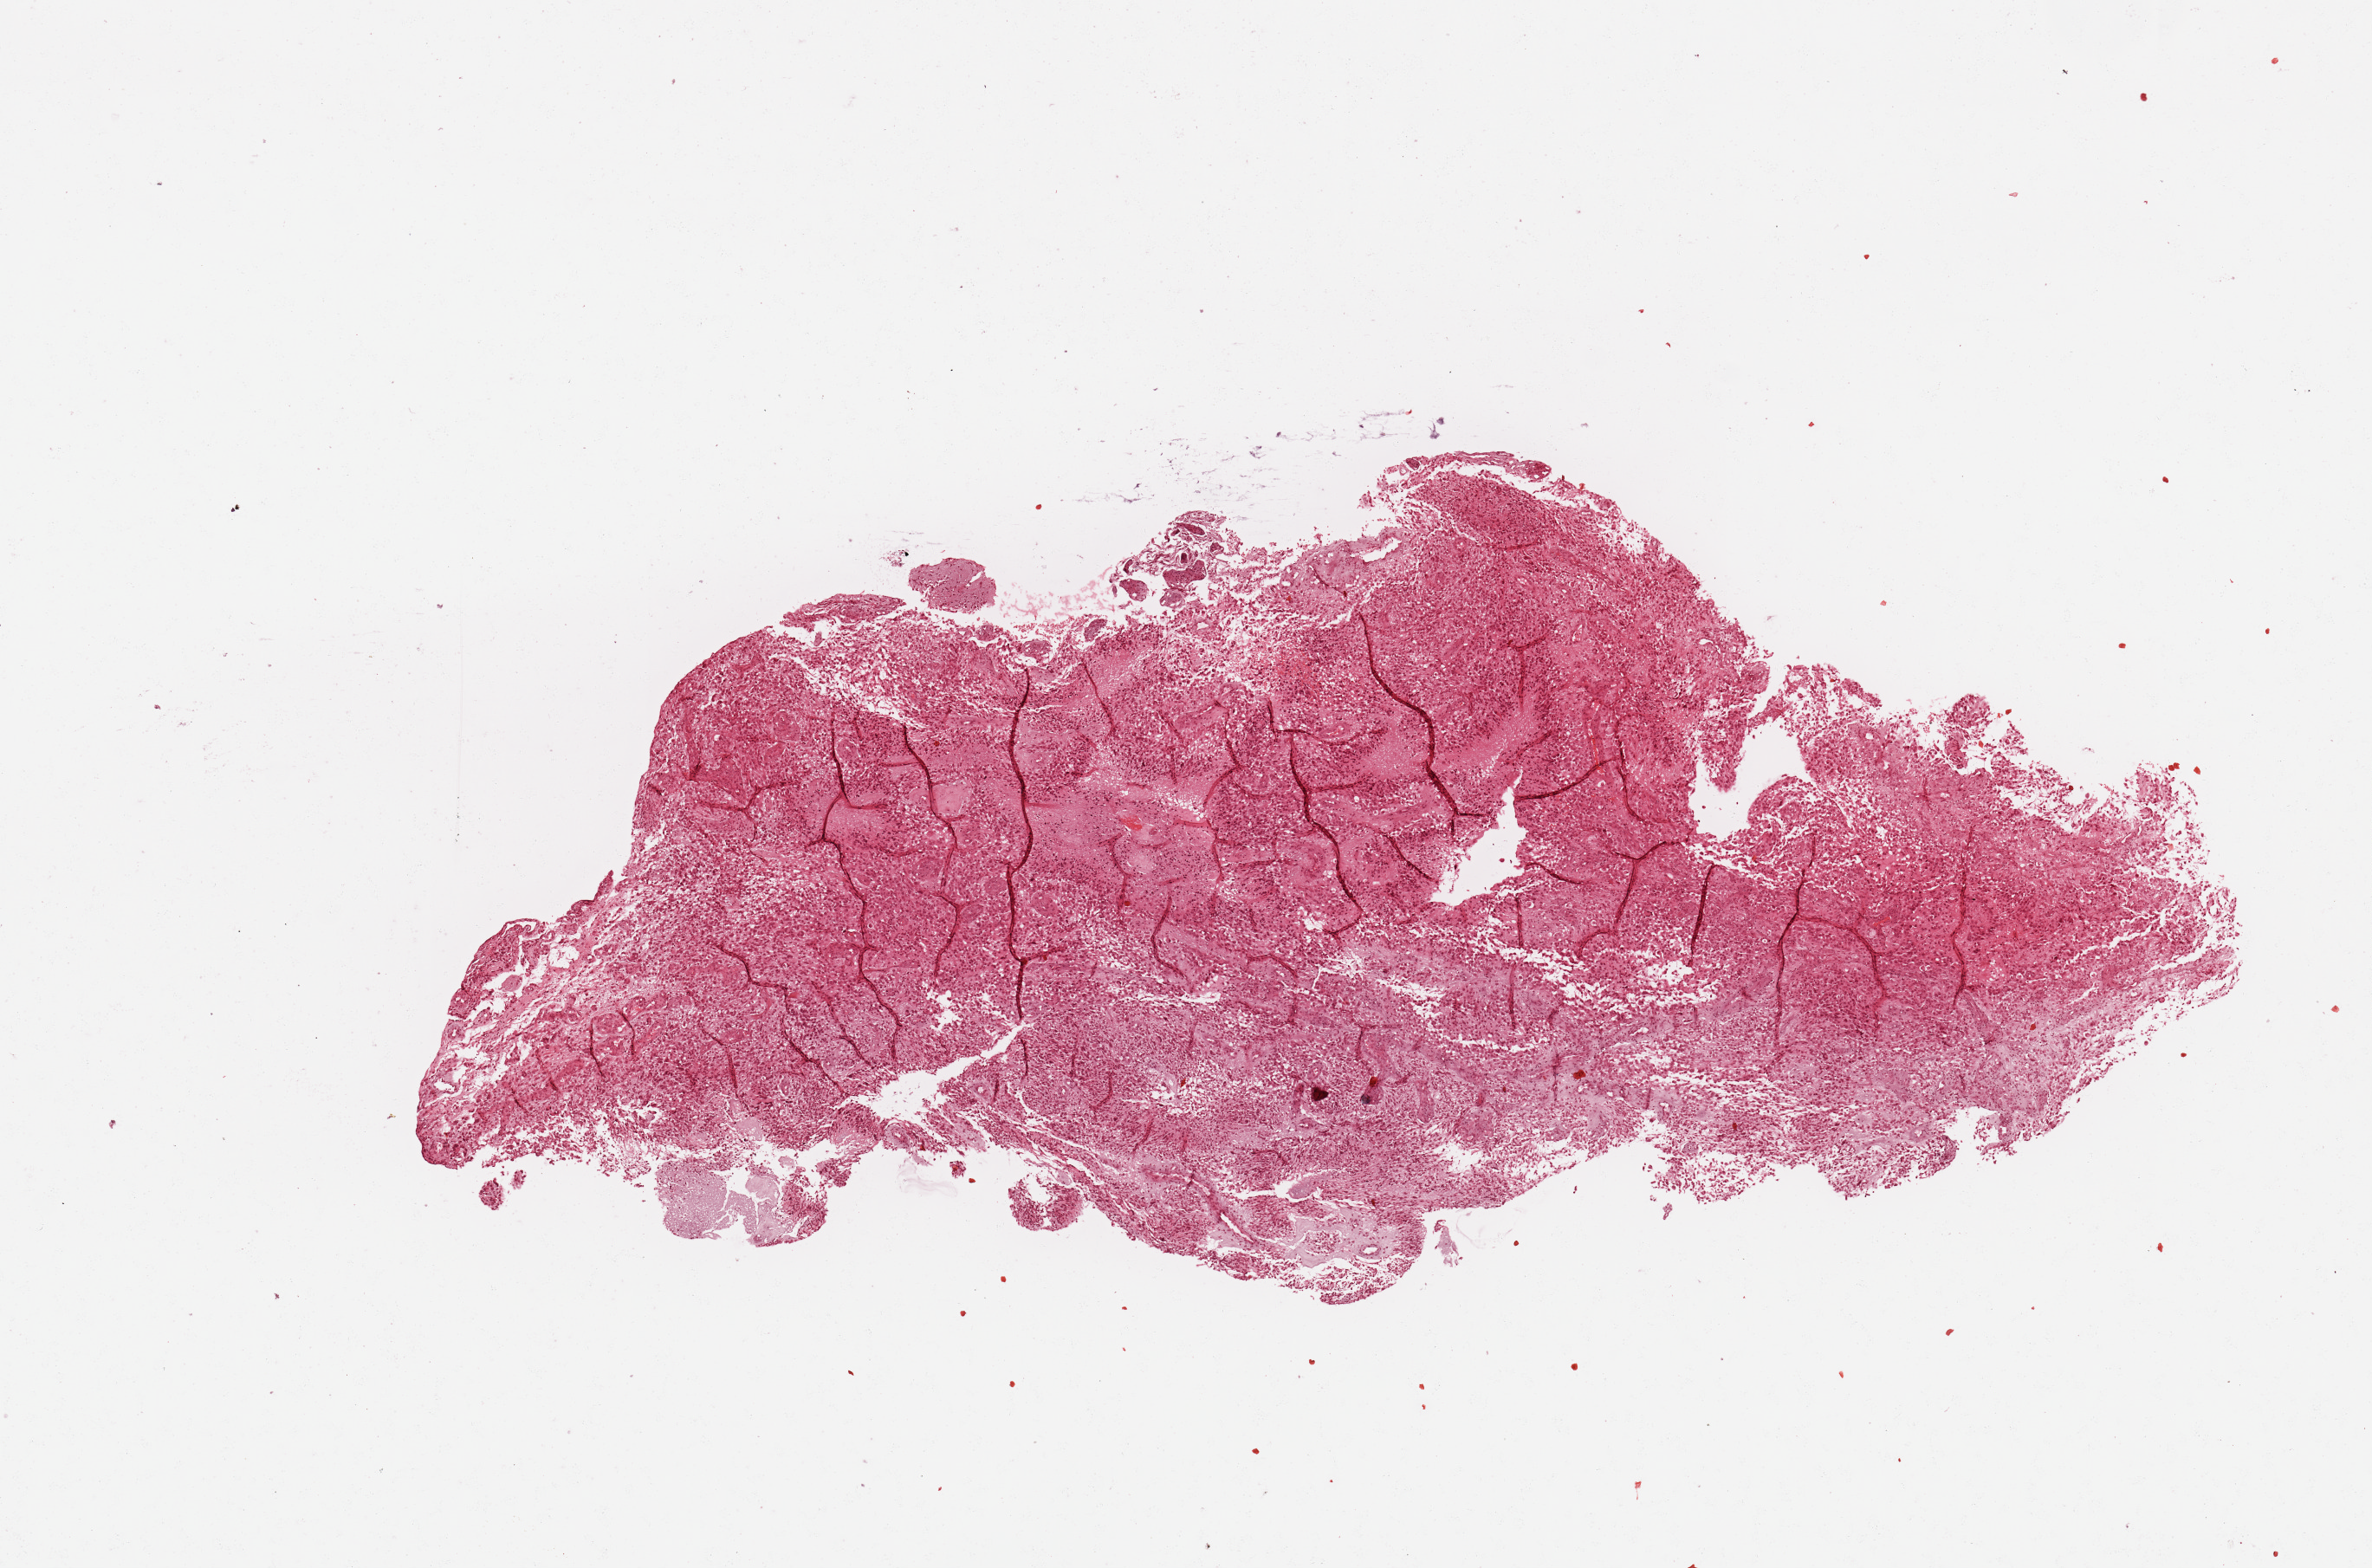
Whole-slide histology image, H&E — low-resolution overview of the scanned area, about 10.8 x 7.2 mm (acquisition: 20x scan). Brain, tumour tissue. Patient: female, age 53 years.
- primary tumour site (as recorded): temporal lobe
- histologic diagnosis: Glioblastoma